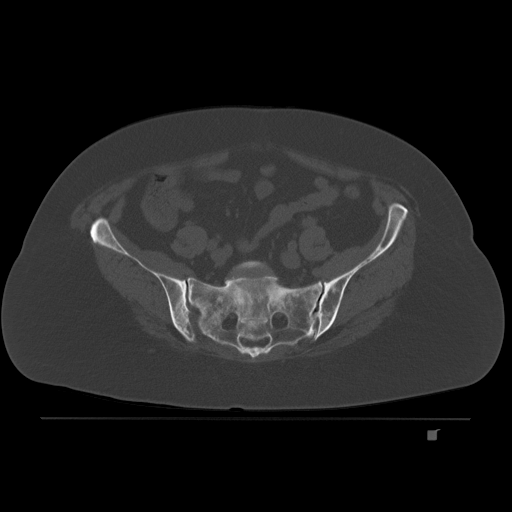
CT including the spine, one axial slice. Position 20 of 221 along the scan axis. Bone window (W 1800 / L 400 HU). 3 mm slice thickness. 512 × 512 image matrix. Patient: female, 63 years. Case-level facts recorded for this patient, not image findings: primary cancer: breast.
Structures marked on this image (semi-automatically segmented with operator editing):
- L5 vertebra: bounding box [x1, y1, x2, y2] px = [231, 260, 269, 273]